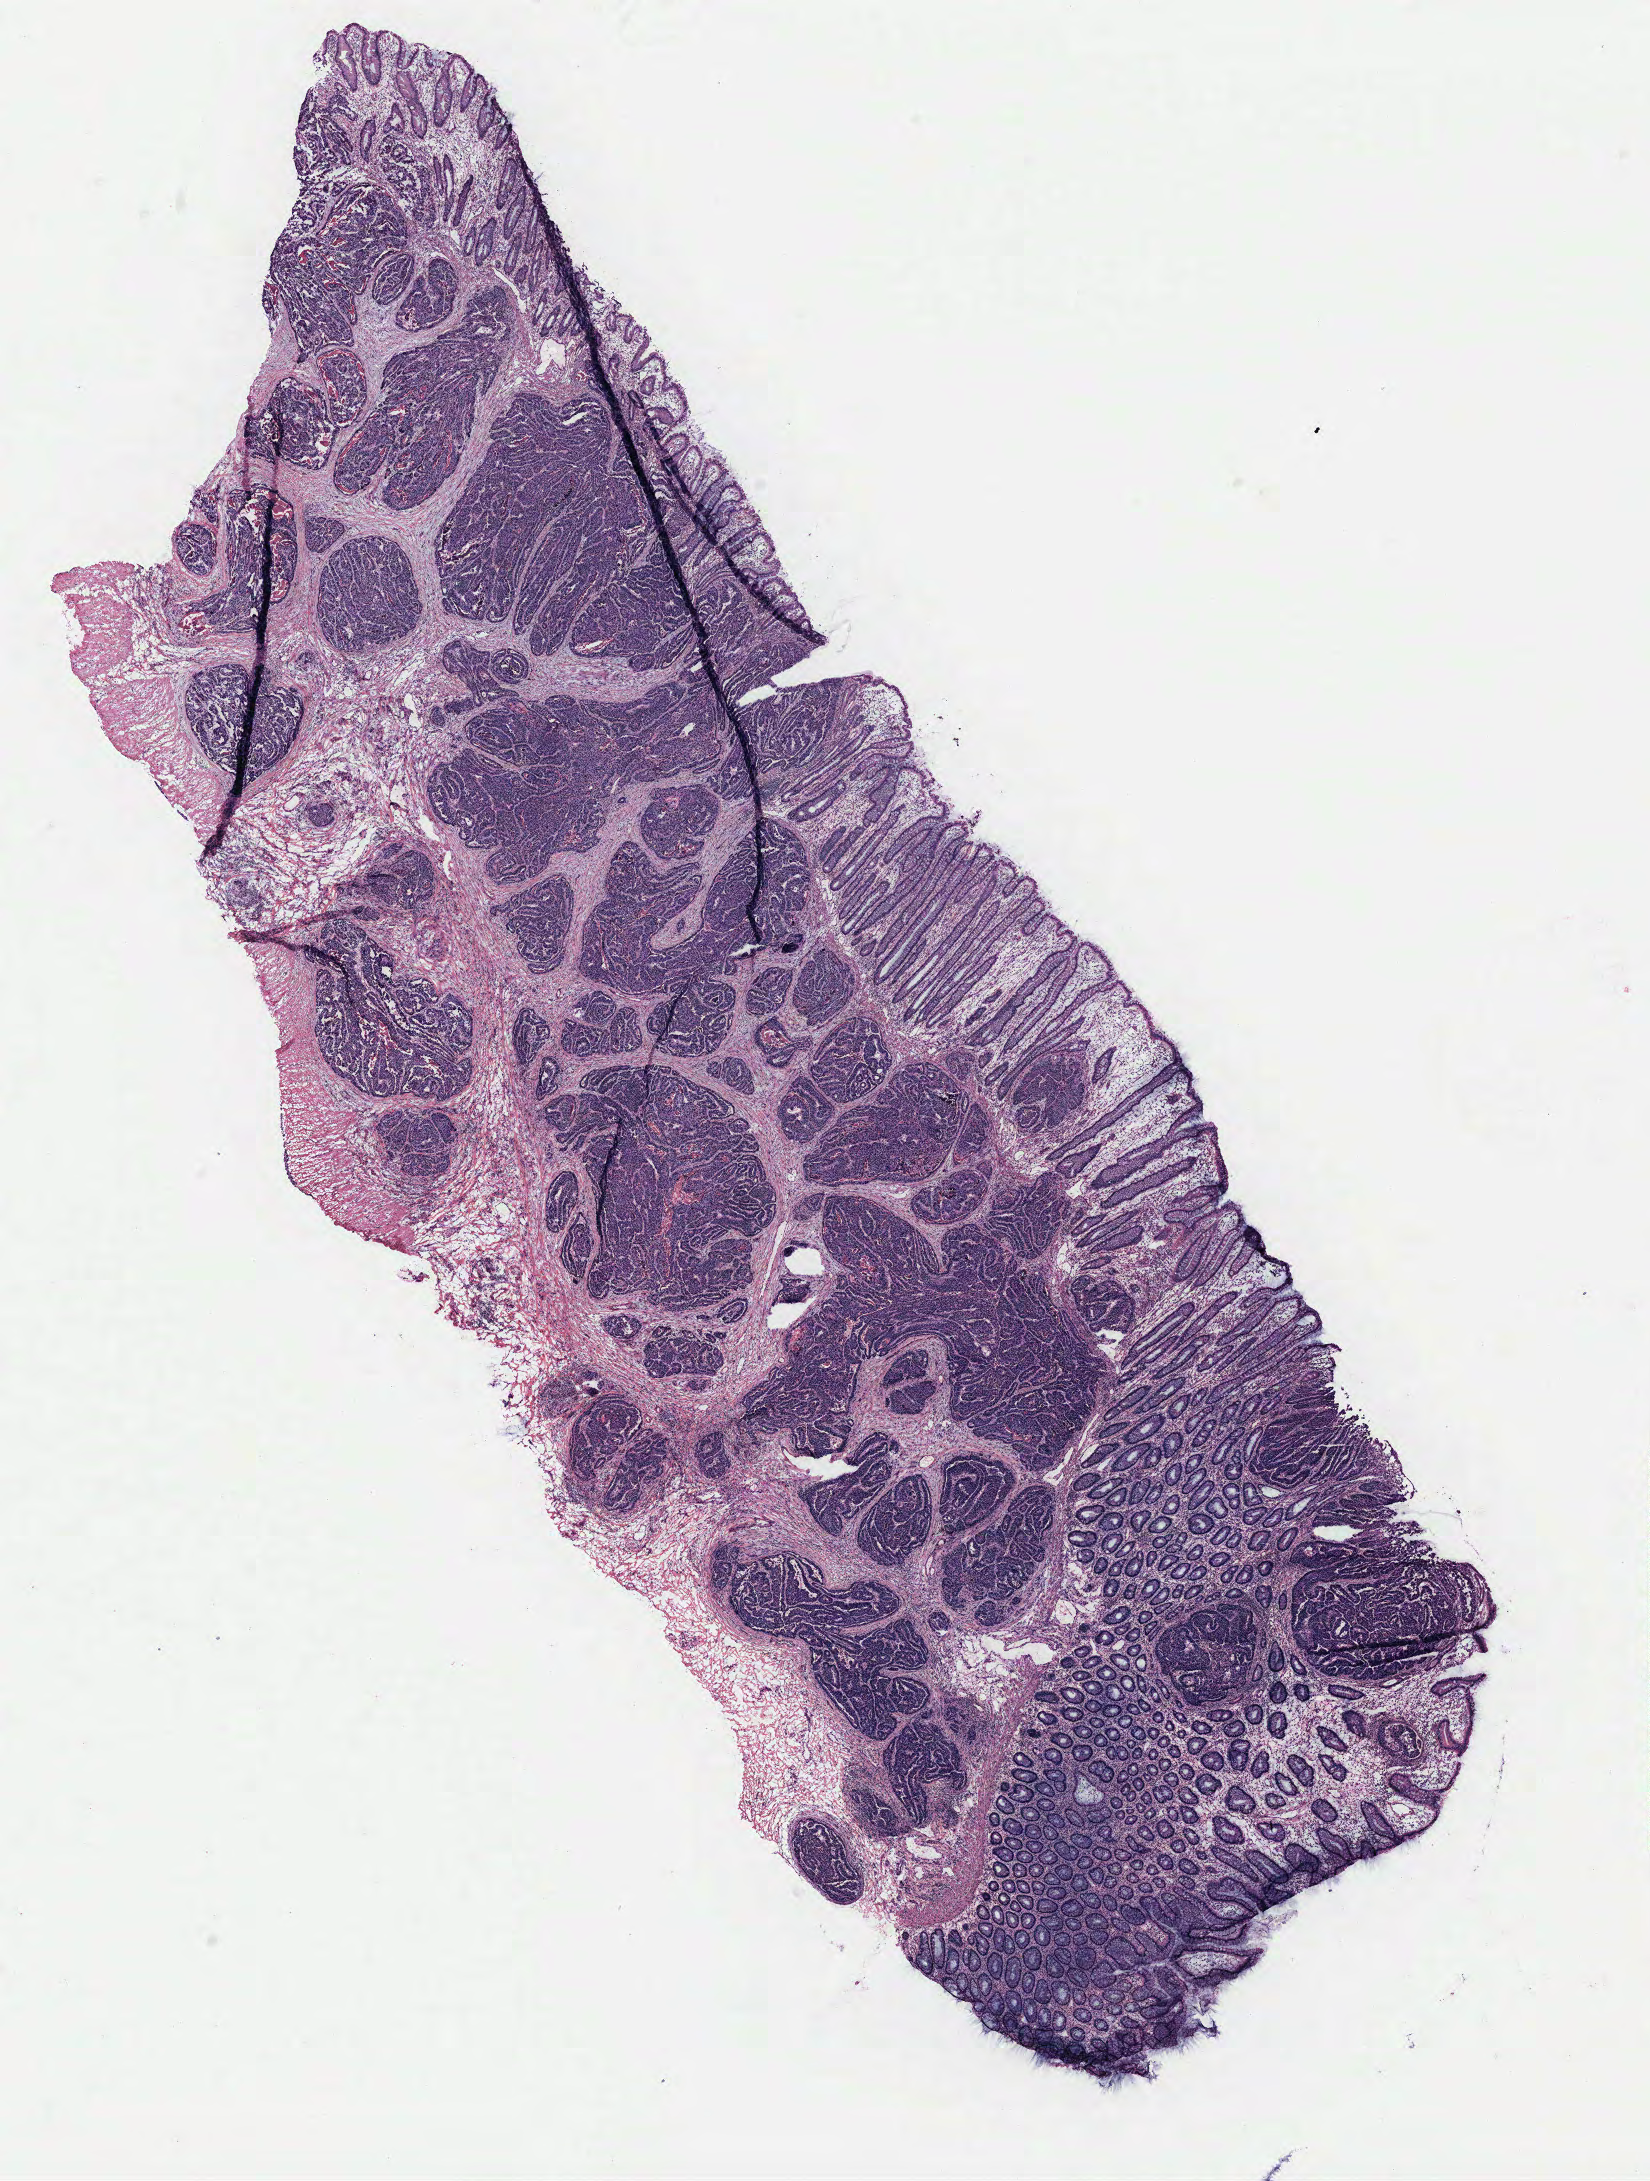
Hematoxylin and eosin (H&E) stained whole-slide image, a low-resolution overview of the entire scanned area, about 13.2 x 17.5 mm (slide scanned at 40x); normal (non-tumour) tissue sample, colon. Male, 39 y/o.
This section: normal (non-tumour) tissue from the same patient. Patient diagnosis: Adenocarcinoma, NOS.